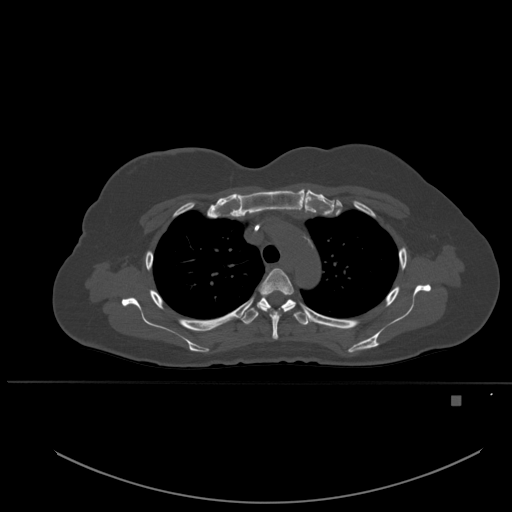
CT including the spine, one axial slice; bone window (W 1800 / L 400 HU); 1.5 mm slice thickness; 512 × 512 image matrix, field of view 443 × 443 mm. Patient: female, 49 years. Case-level facts recorded for this patient, not image findings: primary cancer: breast; vertebrae with lytic lesions (as recorded): L3, T12, L4.
Annotated regions visible in this slice (semi-automatically segmented with operator editing):
- T3 vertebra: box from (x=257, y=268) to (x=295, y=340) px
- T4 vertebra: (x=240, y=294)–(x=308, y=325)